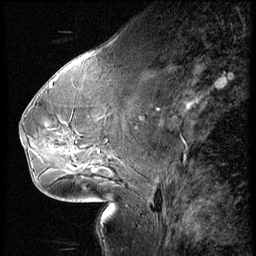
Breast MRI (dynamic contrast-enhanced), one sagittal slice; position 29 of 66 along the scan axis; 3 images stored at this slice position (order not interpretable as contrast timing); 1.5 T; TE 4.2 ms, TR 8.9 ms; 2.5 mm slice thickness; 256 × 256 image matrix, field of view 200 × 200 mm. Patient: female, 54 years. From the clinical record (not read from this slice): setting: breast cancer imaged before/during neoadjuvant chemotherapy; receptor status: HR-positive, HER2-negative.
Outlined on this slice (semi-automatically segmented with operator editing):
- analysis volume of interest (the breast-tissue region the enhancement analysis was run in; not a lesion): bounding box [x1, y1, x2, y2] px = [61, 104, 146, 171]
- tumour enhancement mask (voxels above the 140 % enhancement threshold inside the analysis volume of interest): [97, 150, 99, 153]